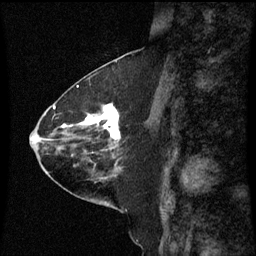
Breast MRI (dynamic contrast-enhanced), one sagittal slice; position 28 of 60 along the scan axis; dynamic contrast-enhanced series, image 2 of 3 at this slice position (ordered by acquisition); 1.5 T; TE 4.2 ms, TR 8.9 ms; 256 × 256 image matrix, field of view 200 × 200 mm. Female patient, age 63 years. From the clinical record (not read from this slice): setting: breast cancer imaged before/during neoadjuvant chemotherapy; receptor status: HR-positive, HER2-negative.
Structures marked on this image (semi-automatically segmented with operator editing):
- analysis volume of interest (the breast-tissue region the enhancement analysis was run in; not a lesion): bounding box <77,104,129,151> (left, top, right, bottom; pixels)
- tumour enhancement mask (voxels above the 70 % enhancement threshold inside the analysis volume of interest): <82,104,120,141>